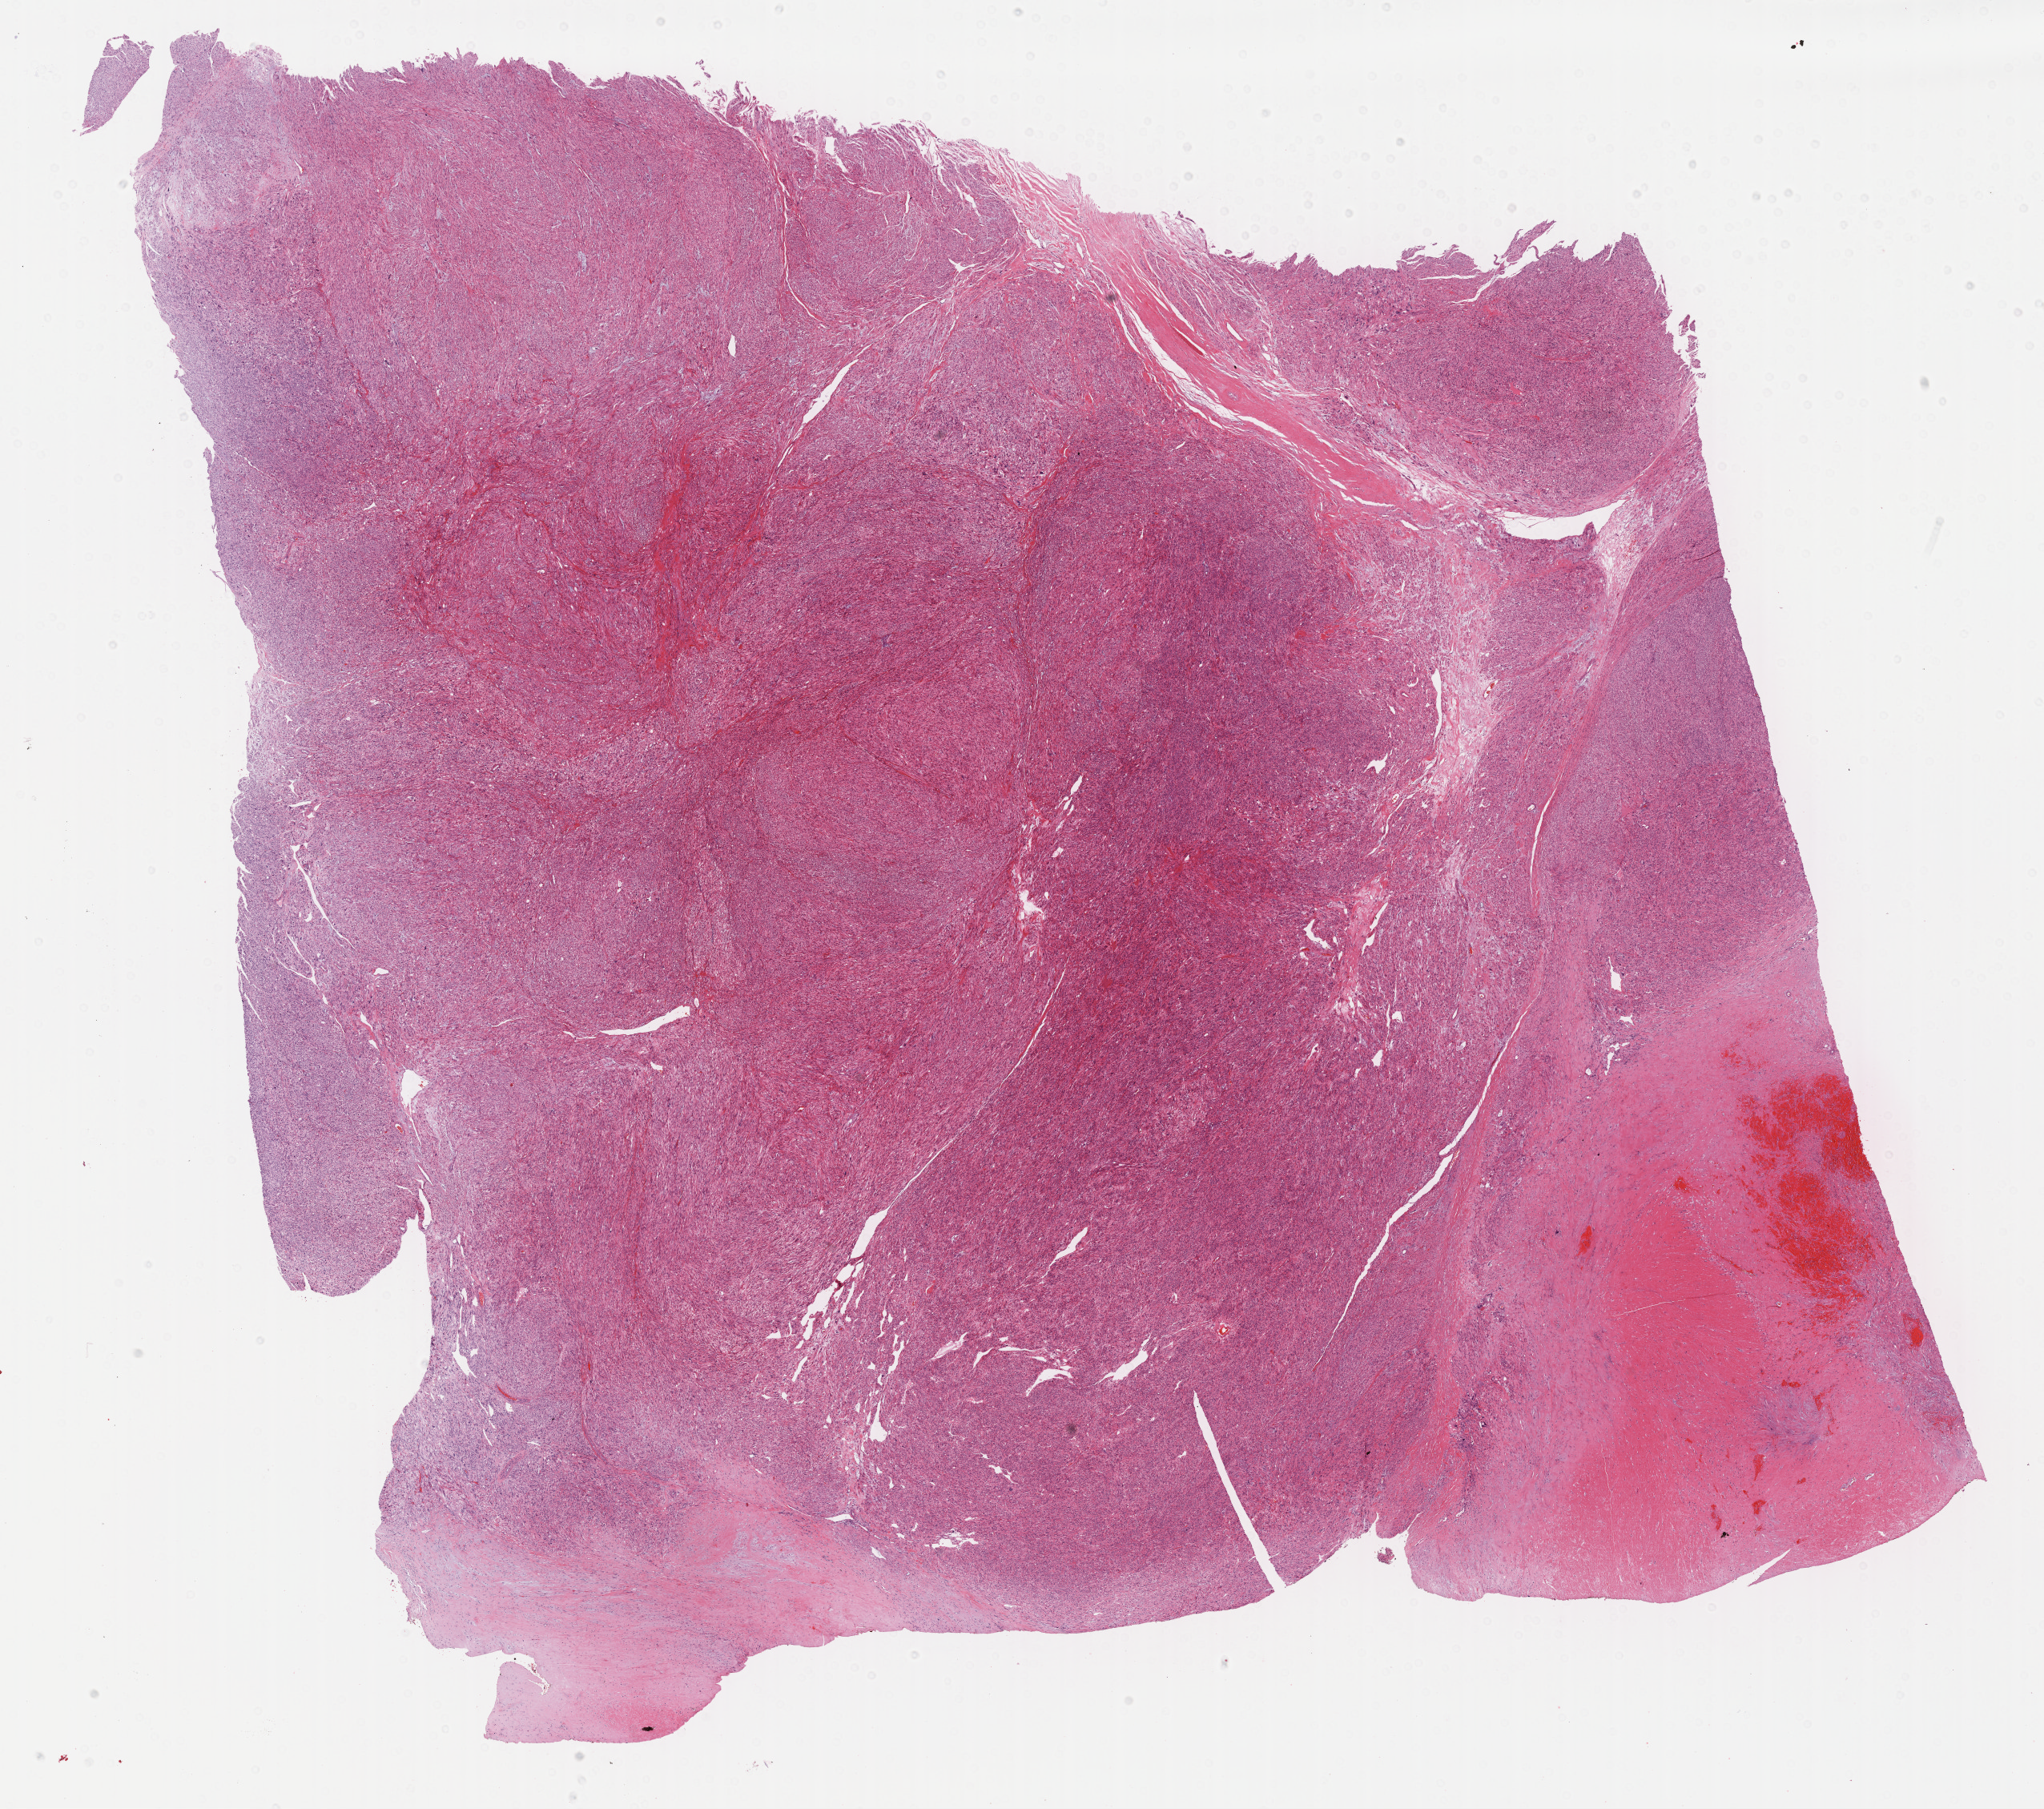
H&E whole-slide image — whole scanned area (about 20.6 x 18.3 mm, from a 40x scan) shown as a low-resolution overview. Formalin-fixed paraffin-embedded (FFPE) diagnostic section. Connective, subcutaneous and other soft tissues, primary tumour sample. Female patient; age at initial diagnosis 56 years.
Diagnosis: Leiomyosarcoma, NOS (connective, subcutaneous and other soft tissues of abdomen).